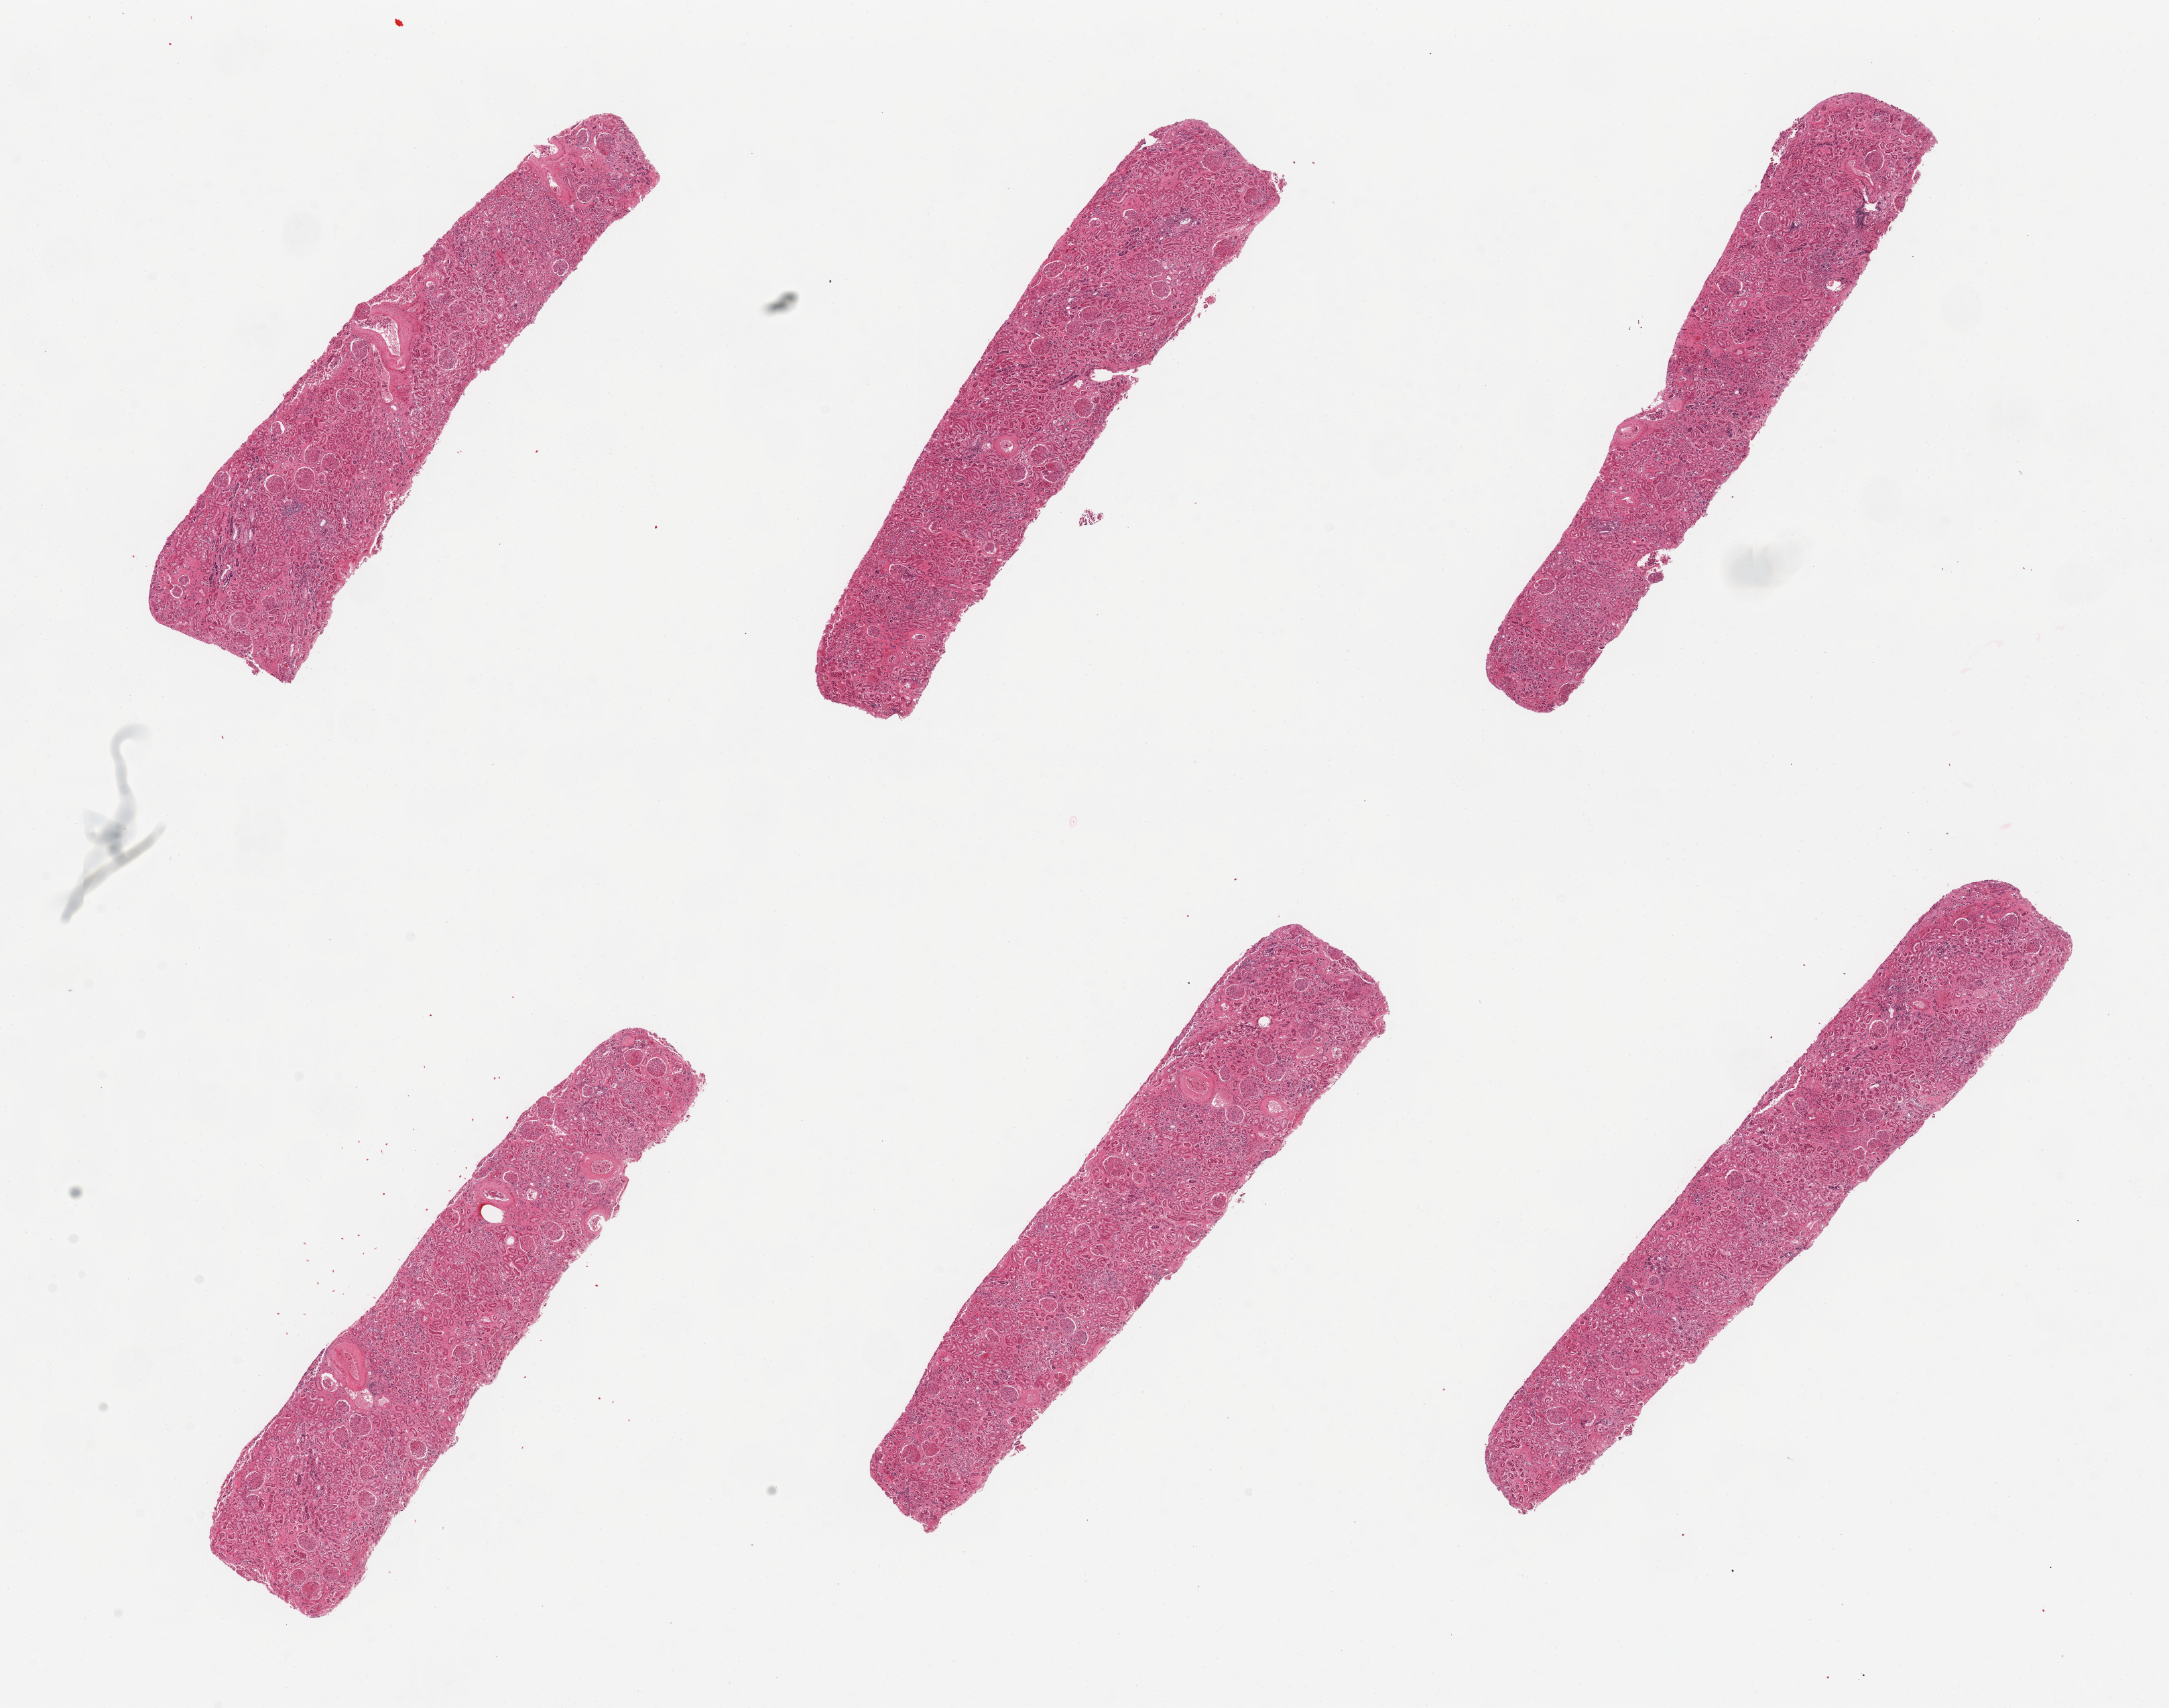
Haematoxylin and eosin whole-slide image, low-resolution overview of the scanned area, about 25.6 x 20.2 mm. PAXgene-fixed, paraffin-embedded tissue. Sampled site (target tissue): renal cortex. Tissue donor sample. Donor: male.
Reviewer comment on this tissue sample: 6 pieces, all cortex.